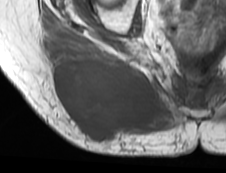
MRI of an extremity soft-tissue mass, one axial slice. Slice 33 of 73 in the series (ordered by position). MR volume resampled by the dataset authors to the PET/CT grid (not the native acquisition matrix). 3.27 mm slice thickness. 226 × 173 image matrix, field of view 221 × 169 mm. Female patient. From the clinical record (not read from this slice): histological type: spindle cell suggestive of myxofibrosarcoma; grade: intermediate; site of the primary tumour: right buttock.
Outlined on this slice (expert contour drawn on MRI and transferred to this co-registered scan by the dataset authors):
- gross tumour volume (mass): bounding box (x1, y1, x2, y2) in pixels: (49, 44, 158, 143)